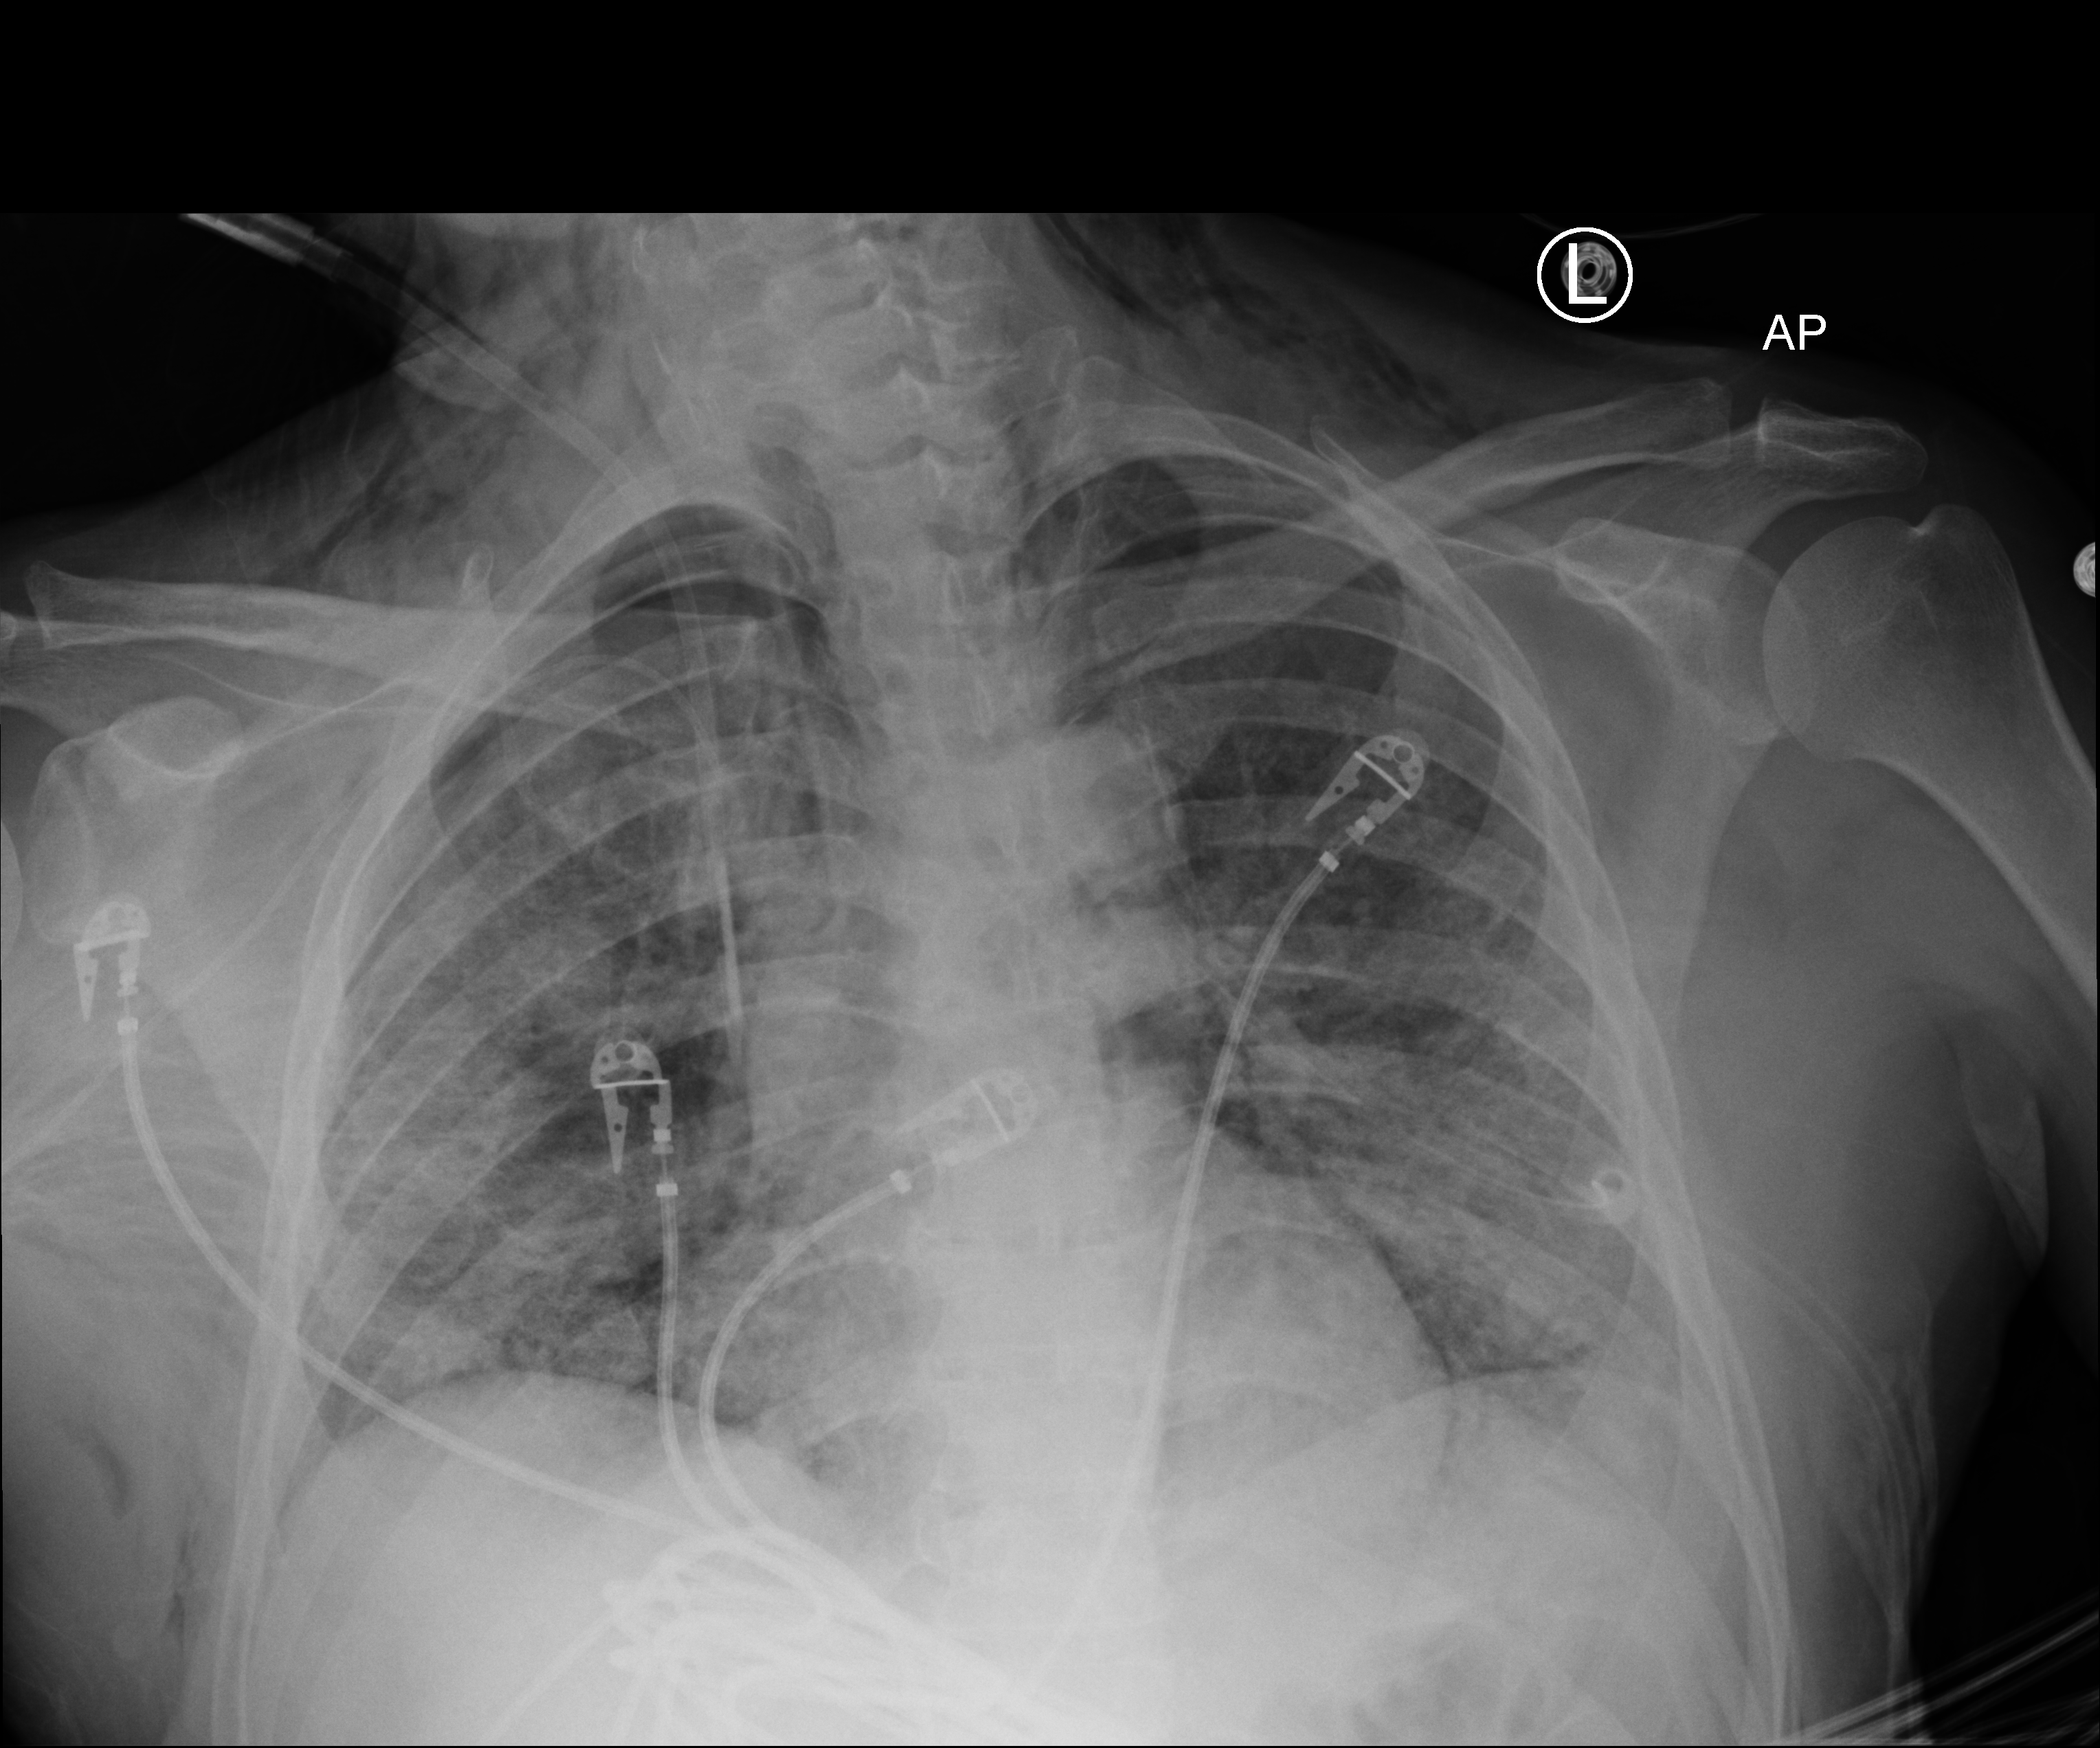
Portable chest radiograph, anteroposterior (AP) projection. Male patient hospitalised with COVID-19, age 18–59 years.
Admission-level facts for this patient (not findings on this image; timing relative to this image not recorded):
- diabetes (admission record): no
- mechanically ventilated during this hospital stay: yes